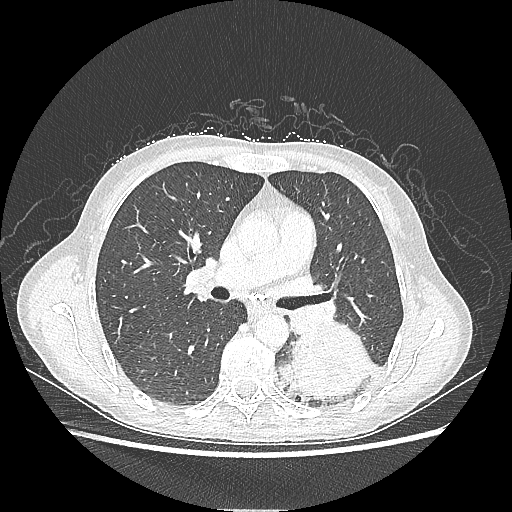
Chest CT, one axial slice. Slice 127 of 220 in the series (ordered by position). Lung window (W 1500 / L -600 HU). 1.25 mm slice thickness. 512 × 512 image matrix, field of view 360 × 360 mm. Patient: female, 53 years. From the clinical record (not read from this slice): clinical TNM (as recorded): T3 N0 M0.
Annotated regions visible in this slice (rectangle marked by the reading radiologist):
- lung tumour (recorded histology: adenocarcinoma): box from (x=283, y=325) to (x=375, y=398) px